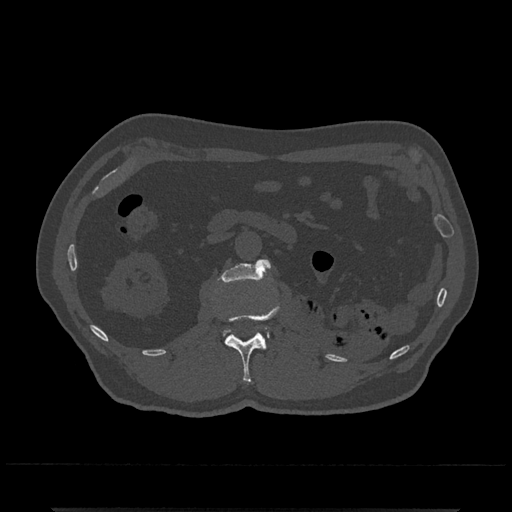
CT including the spine, one axial slice; position 336 of 797 along the scan axis; 120 kVp; bone window (W 1800 / L 400 HU); 512 × 512 image matrix. Patient: male, 67 years. Case-level facts recorded for this patient, not image findings: primary cancer: prostate.
Annotated regions visible in this slice (semi-automatically segmented with operator editing):
- L1 vertebra: bounding box [x1, y1, x2, y2] px = [225, 306, 279, 383]
- L2 vertebra: [218, 259, 271, 340]